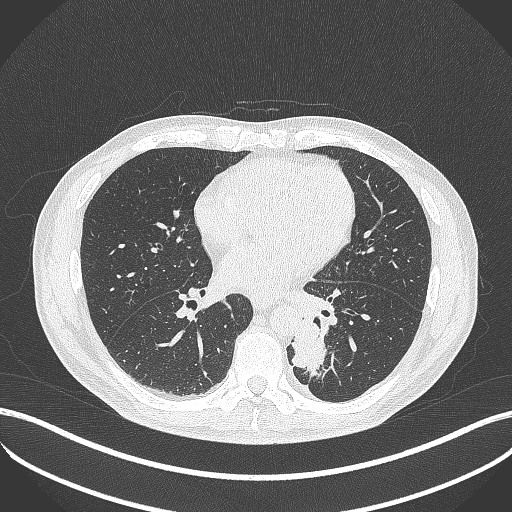
Chest CT, one axial slice. Slice 176 of 451 in the series (ordered by position). Reconstruction kernel B70f. 120 kVp. Lung window (W 1500 / L -600 HU). 1 mm slice thickness. 512 × 512 image matrix, field of view 400 × 400 mm. Male patient, age 72 years. From the clinical record (not read from this slice): clinical TNM (as recorded): T2b N0 M1.
Structures marked on this image (rectangle marked by the reading radiologist):
- lung tumour (recorded histology: adenocarcinoma): bounding box <287,315,329,377> (left, top, right, bottom; pixels)